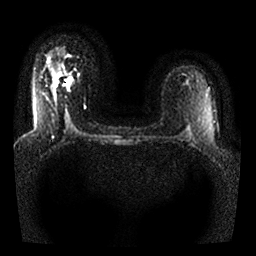
Breast MRI, one axial slice. Diffusion-weighted series; image 2 of 4 stored at this slice position (different b-values; order by instance number). 1.5 T. 4 mm slice thickness. 256 × 256 image matrix. Female patient.
Outlined on this slice (outlined manually by an expert reader):
- tumour on diffusion-weighted imaging: box from (x=67, y=77) to (x=72, y=85) px